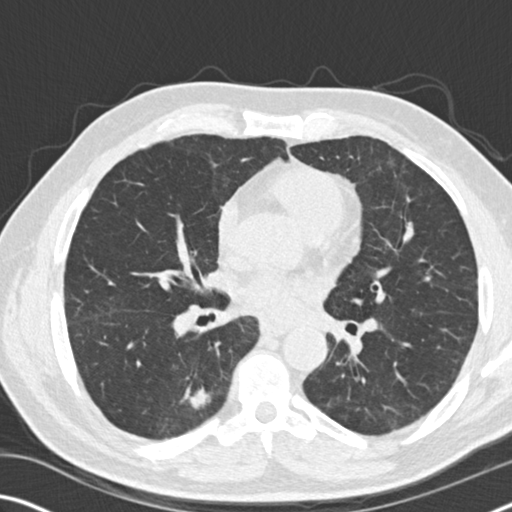
Chest CT (low-dose screening protocol), one axial image. First (baseline) screen. Lung window (W 1500 / L -600 HU). 2 mm slice thickness. Male, age 71 years at enrolment. Current smoker at enrolment.
Expert-annotated lung lesion, bounding box [x1, y1, x2, y2] px = [159, 370, 229, 433]. The screening reader recorded 2 non-calcified nodules or masses ≥4 mm on this exam (right lower lobe, left lower lobe); which of them this box marks is not recorded. Official screen result: positive, change unspecified: nodule(s) >= 4 mm or enlarging nodule(s), mass(es), or other non-specific abnormalities suspicious for lung cancer. Later outcome: lung cancer diagnosed 215 days after this screen — squamous cell carcinoma, NOS, right lower lobe, moderately differentiated (G2), stage IB (AJCC 6th edition), 52 mm at pathology.